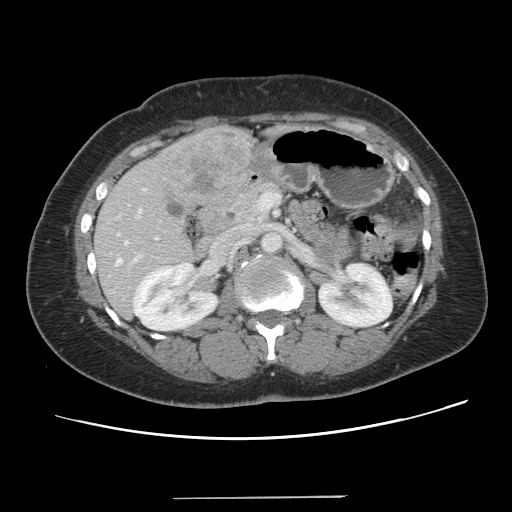
Contrast-enhanced abdominal CT, one axial slice. Position 59 of 141 along the scan axis. 120 kVp. Intravenous contrast given. Soft-tissue window (W 400 / L 40 HU). 2.5 mm slice thickness. 512 × 512 image matrix, field of view 366 × 366 mm. Female patient, age 53 years. From the clinical record (not read from this slice): diagnosis: colorectal cancer liver metastases, imaged before liver resection; multiple liver metastases: no; largest metastasis: 14.5 cm; disease in both lobes: yes.
Outlined on this slice (manually delineated by an expert):
- hepatic veins: bounding box [x1, y1, x2, y2] px = [115, 241, 127, 265]
- liver: [95, 127, 250, 318]
- planned liver remnant (the part of the liver to remain after resection): [95, 215, 193, 317]
- portal vein (with intrahepatic branches): [134, 210, 156, 260]
- liver metastasis: [165, 132, 242, 198]